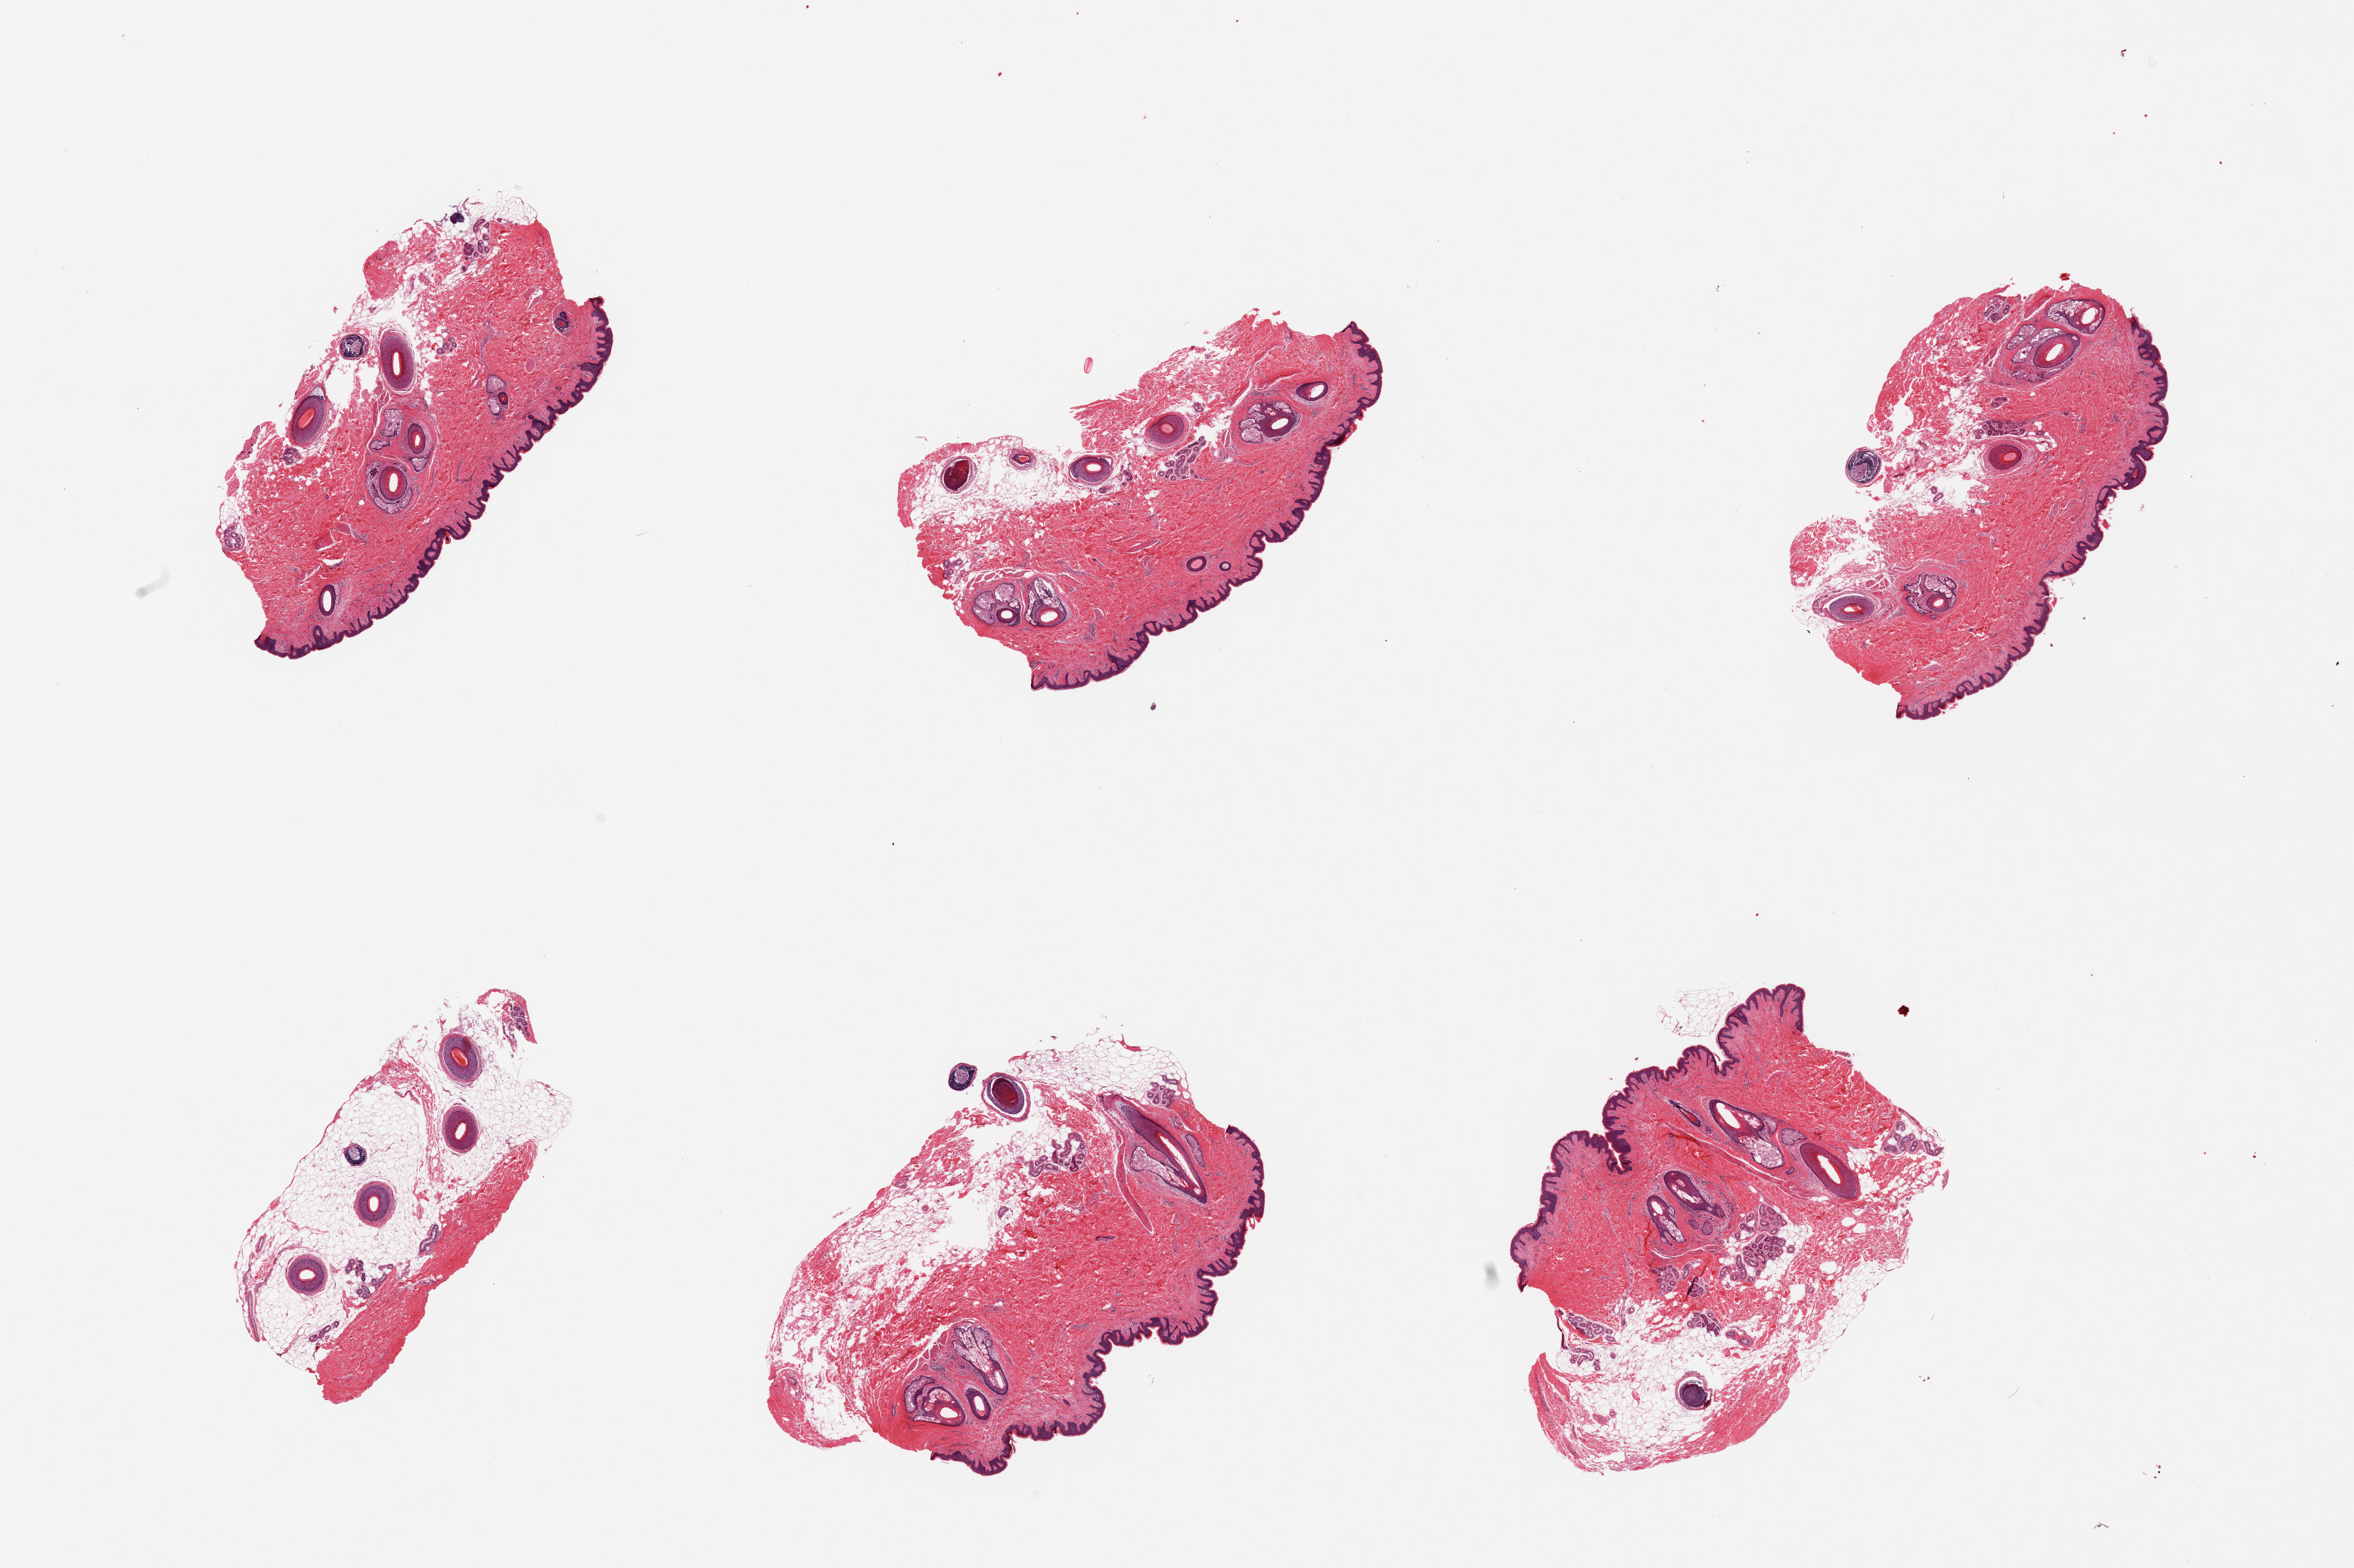
Whole-slide image, hematoxylin and eosin (H&E) stain, brightfield, low-resolution overview of the scanned area, about 24.6 x 16.4 mm, PAXgene-fixed, paraffin-embedded tissue, sampled site (target tissue): skin of suprapubic region, tissue donor sample. Donor: male.
Reviewer comment on this tissue sample: 6 pieces; hair-bearing skin sampled (not target); 20-50% intradermal and subcutaneous adipose tissue.